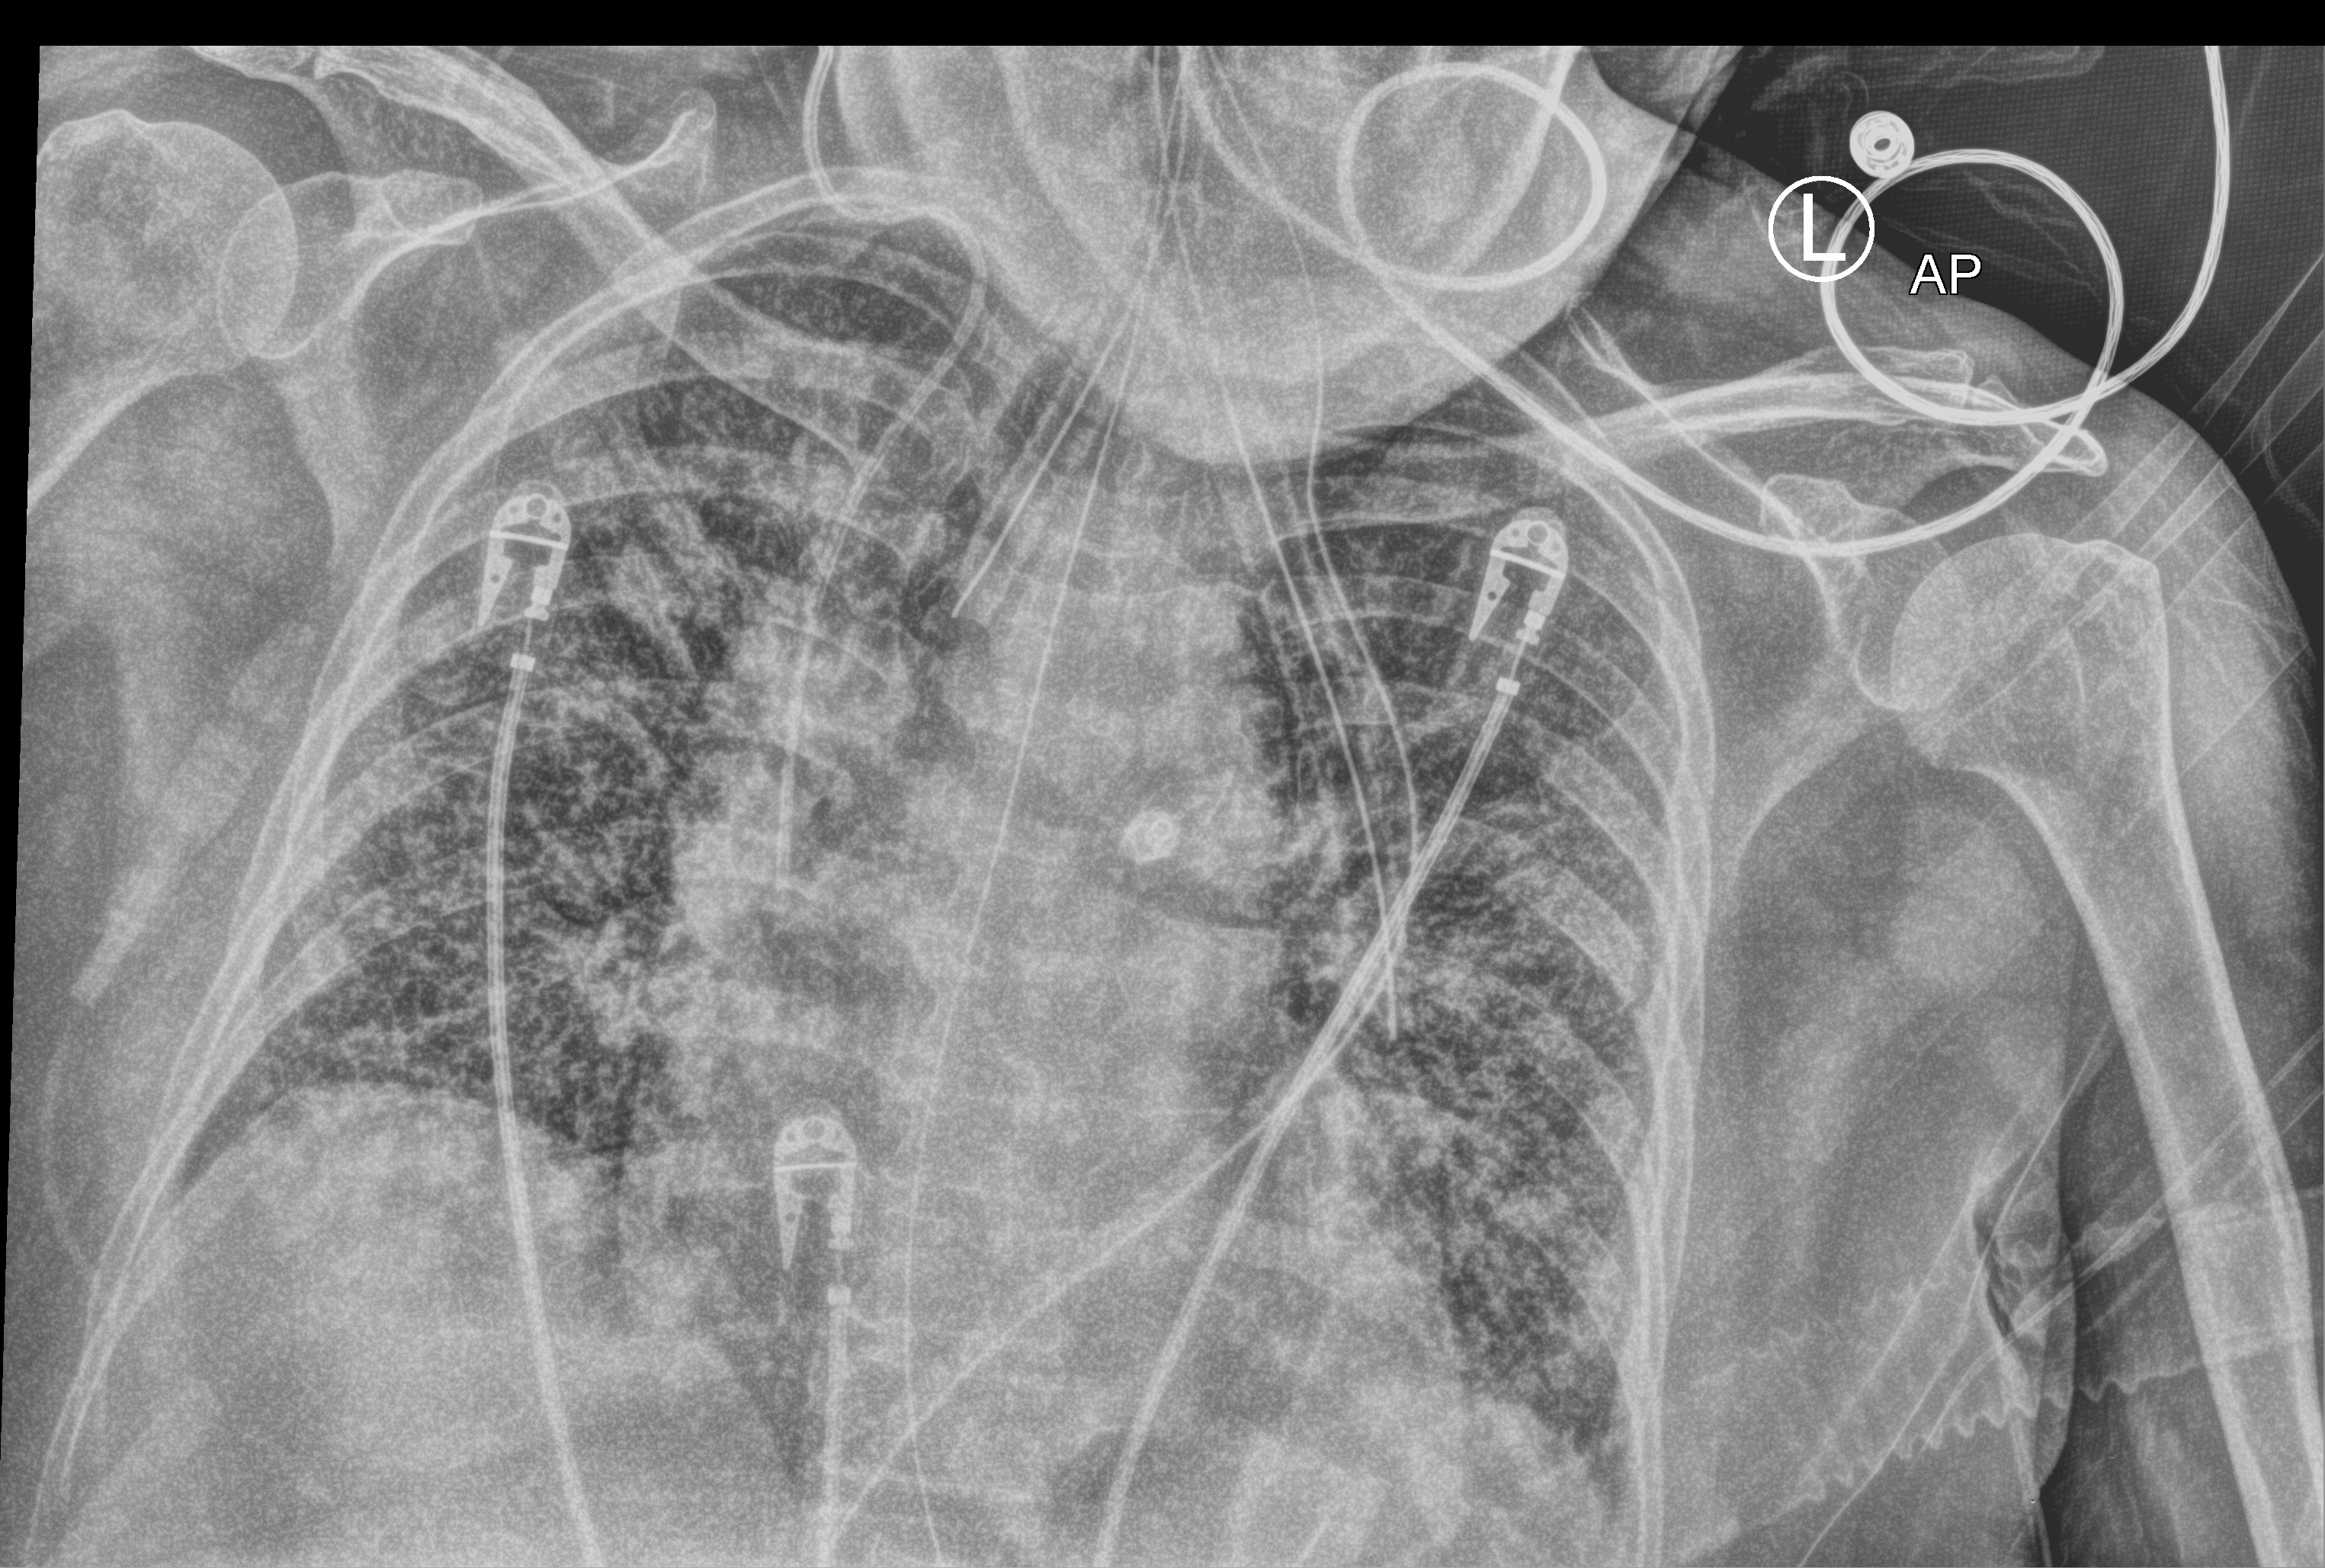
Chest X-ray (portable), anteroposterior (AP) projection. Female patient hospitalised with COVID-19, age 60–74 years.
Hospital-stay facts (about this admission, not read from this image; timing relative to this image not recorded): chronic kidney disease (admission record): no; mechanically ventilated during this hospital stay: yes.